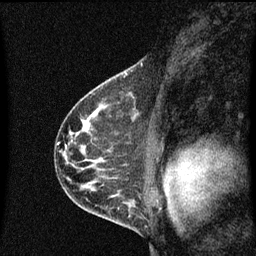
Breast MRI (dynamic contrast-enhanced), one sagittal slice; slice 42 of 60 in the series (ordered by position); dynamic contrast-enhanced series, image 2 of 3 at this slice position (ordered by acquisition); 1.5 T; TE 4.2 ms, TR 8.4 ms; 2 mm slice thickness; 256 × 256 image matrix, field of view 200 × 200 mm. Patient: female, 41 years.
Structures marked on this image (semi-automatic segmentation, software-assisted and operator-edited):
- analysis volume of interest (the breast-tissue region the enhancement analysis was run in; not a lesion): box from (x=121, y=74) to (x=144, y=99) px
- tumour enhancement mask (voxels above the 70 % enhancement threshold inside the analysis volume of interest): (x=125, y=74)–(x=128, y=77)